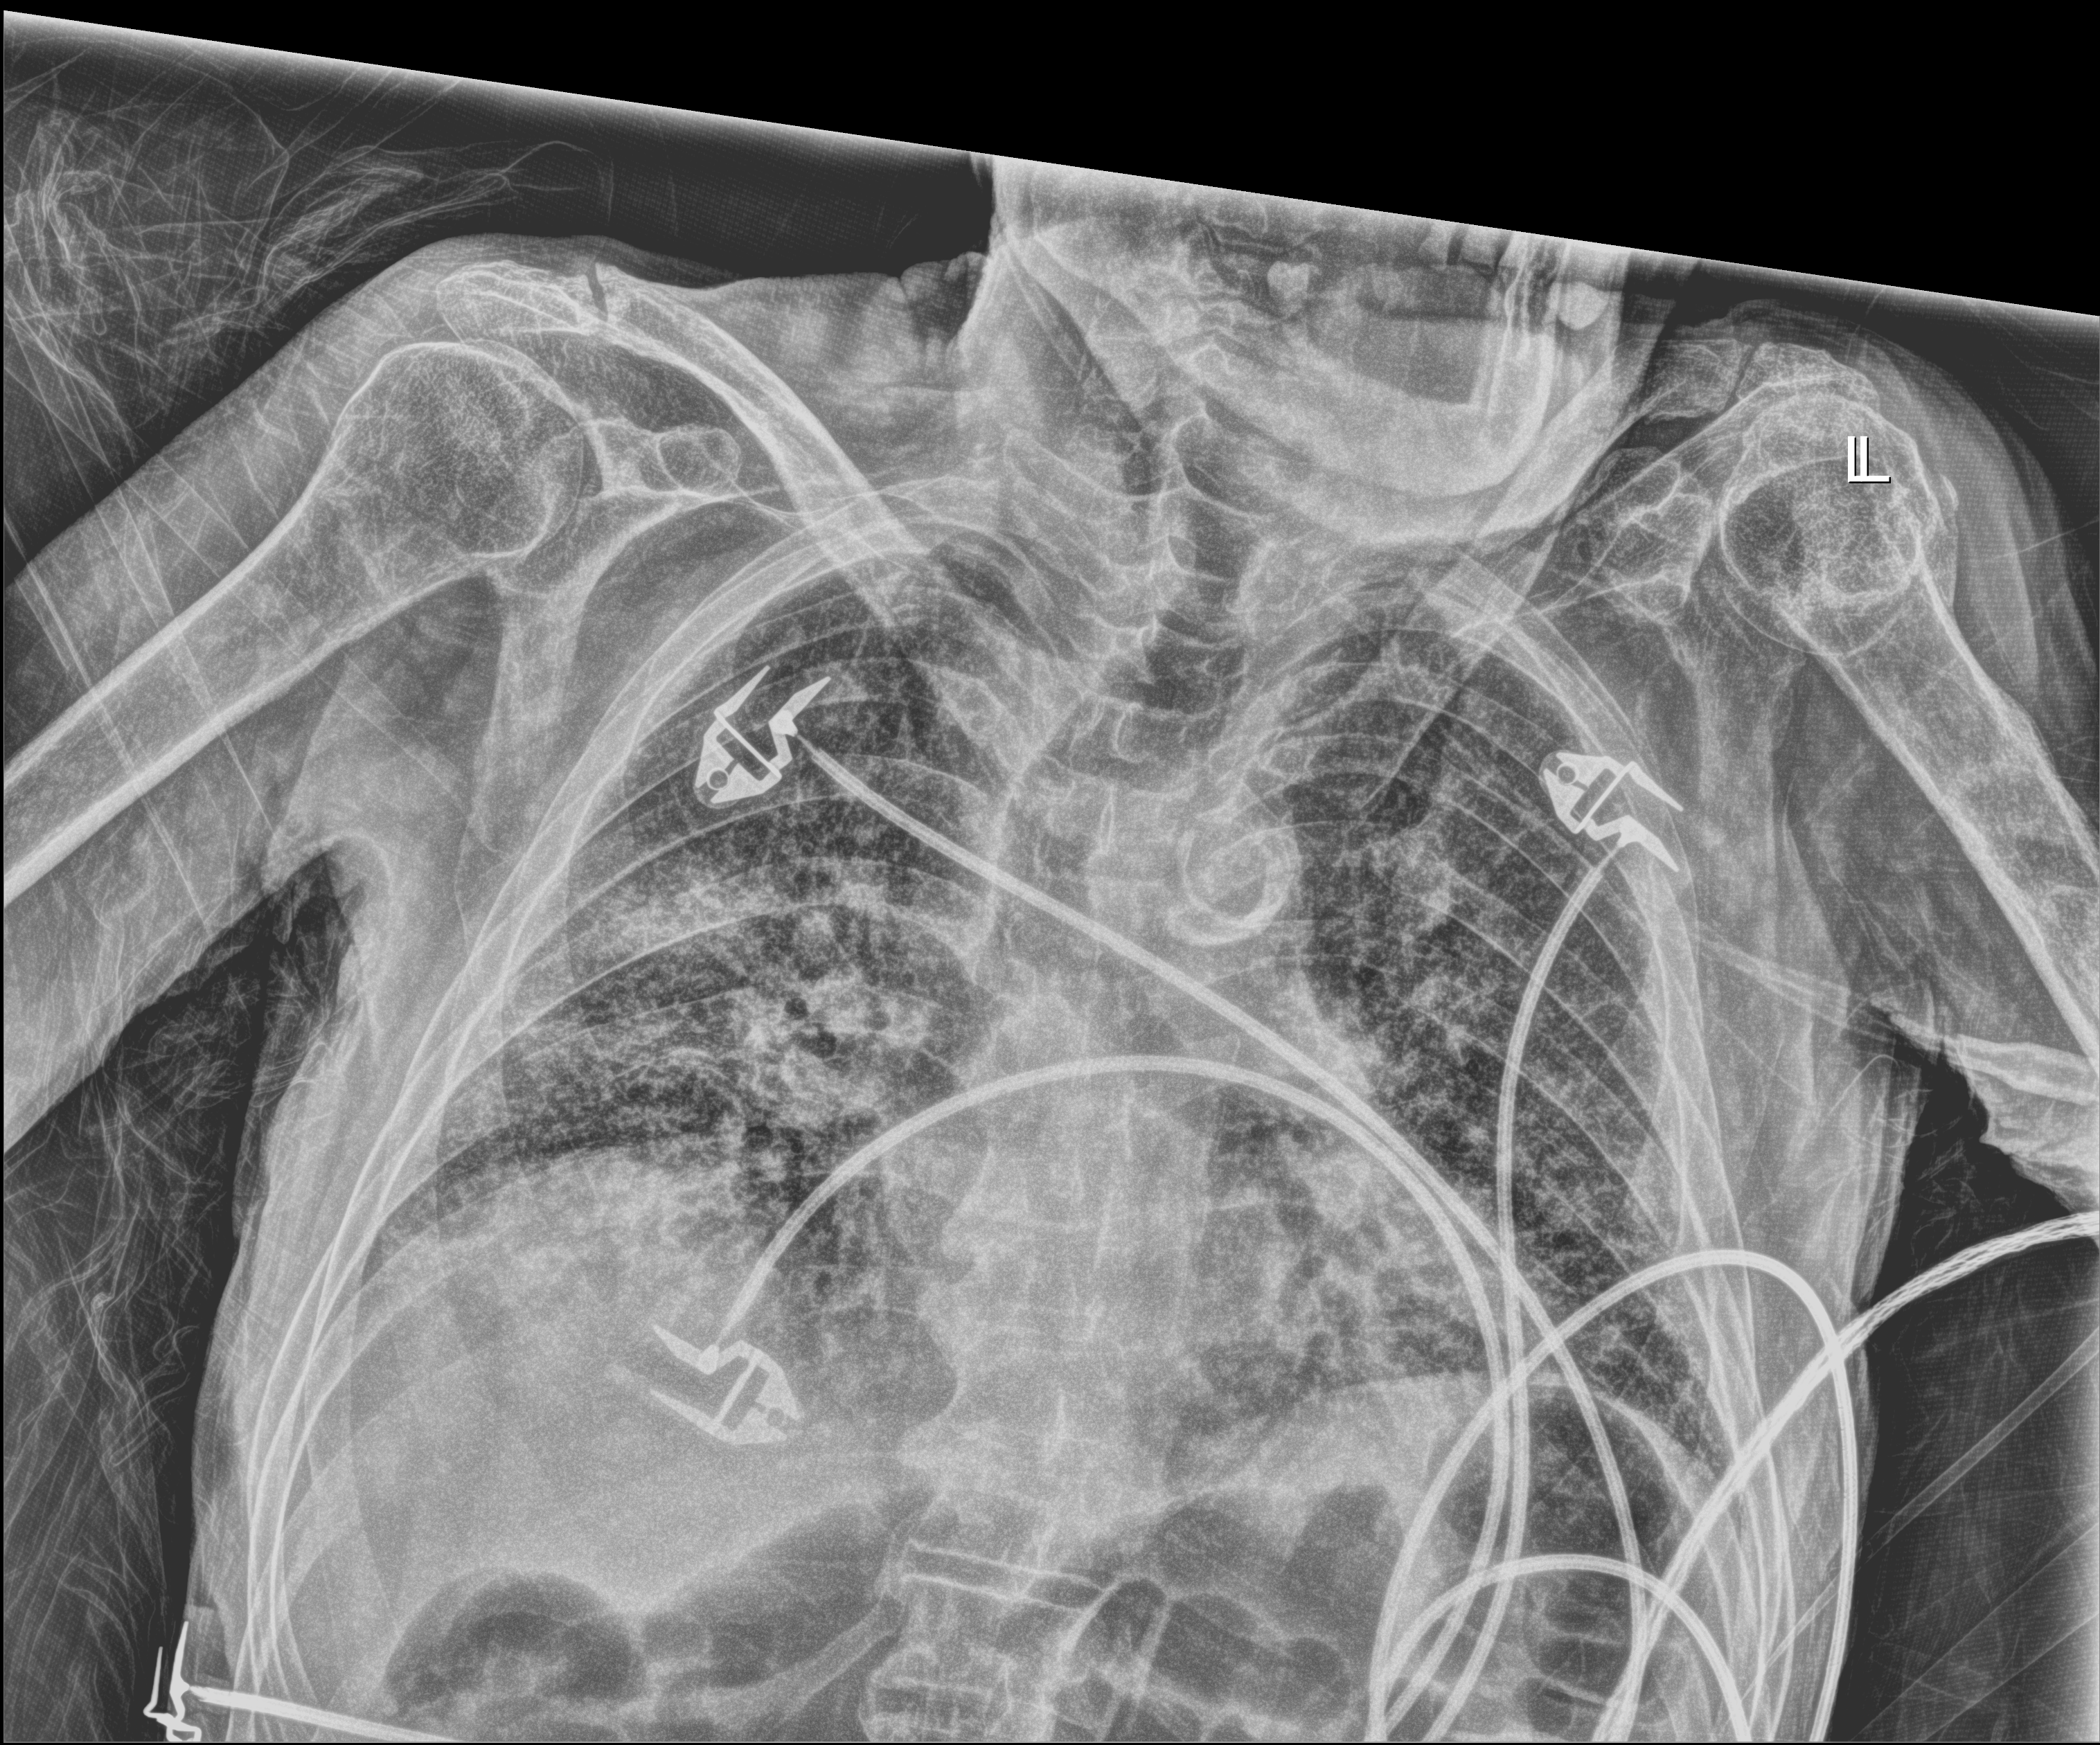
Chest radiograph (digital radiography); anteroposterior (AP) projection. Patient hospitalised with COVID-19; male, aged 60–74 years.
From the hospital-stay record, not from the radiograph (when in the stay this image was taken is not recorded): admitted to intensive care during this hospital stay: no; length of hospital stay: 20 days.